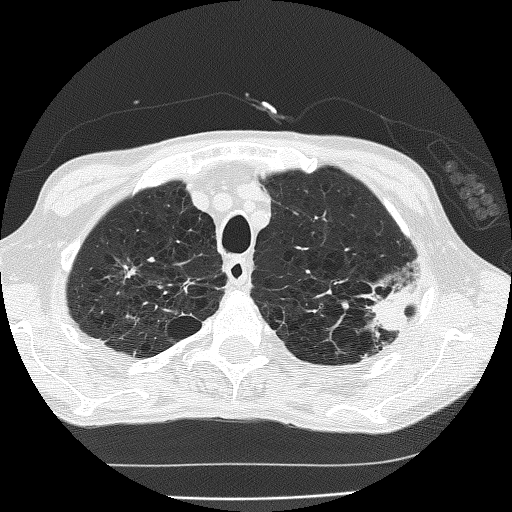
Chest CT (low-dose screening protocol), one axial image, second screening round (one year after baseline), lung window (W 1500 / L -600 HU), lung (sharp) reconstruction kernel (FC51). Male participant, aged 60 years at enrolment. Current smoker at enrolment.
- Expert-annotated lung lesion, bounding box (x1, y1, x2, y2) in pixels: (346, 271, 421, 342).
- The screening reader recorded 2 non-calcified nodules or masses ≥4 mm on this exam (left upper lobe, left upper lobe); which of them this box marks is not recorded.
- Official screen result: positive, other.
- Later outcome: lung cancer diagnosed 178 days after this screen — bronchiolo-alveolar carcinoma, mucinous, left upper lobe, stage IV (AJCC 6th edition).